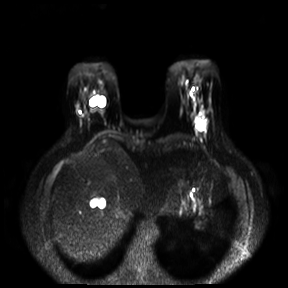
Breast MRI, one axial slice; slice 5 of 30 in the series (ordered by position); diffusion-weighted series; image 2 of 4 stored at this slice position (different b-values; order by instance number); 3 T; 288 × 288 image matrix, field of view 360 × 360 mm. Female patient.
Annotated regions visible in this slice (outlined manually by an expert reader):
- tumour on diffusion-weighted imaging: bounding box <196,116,206,126> (left, top, right, bottom; pixels)